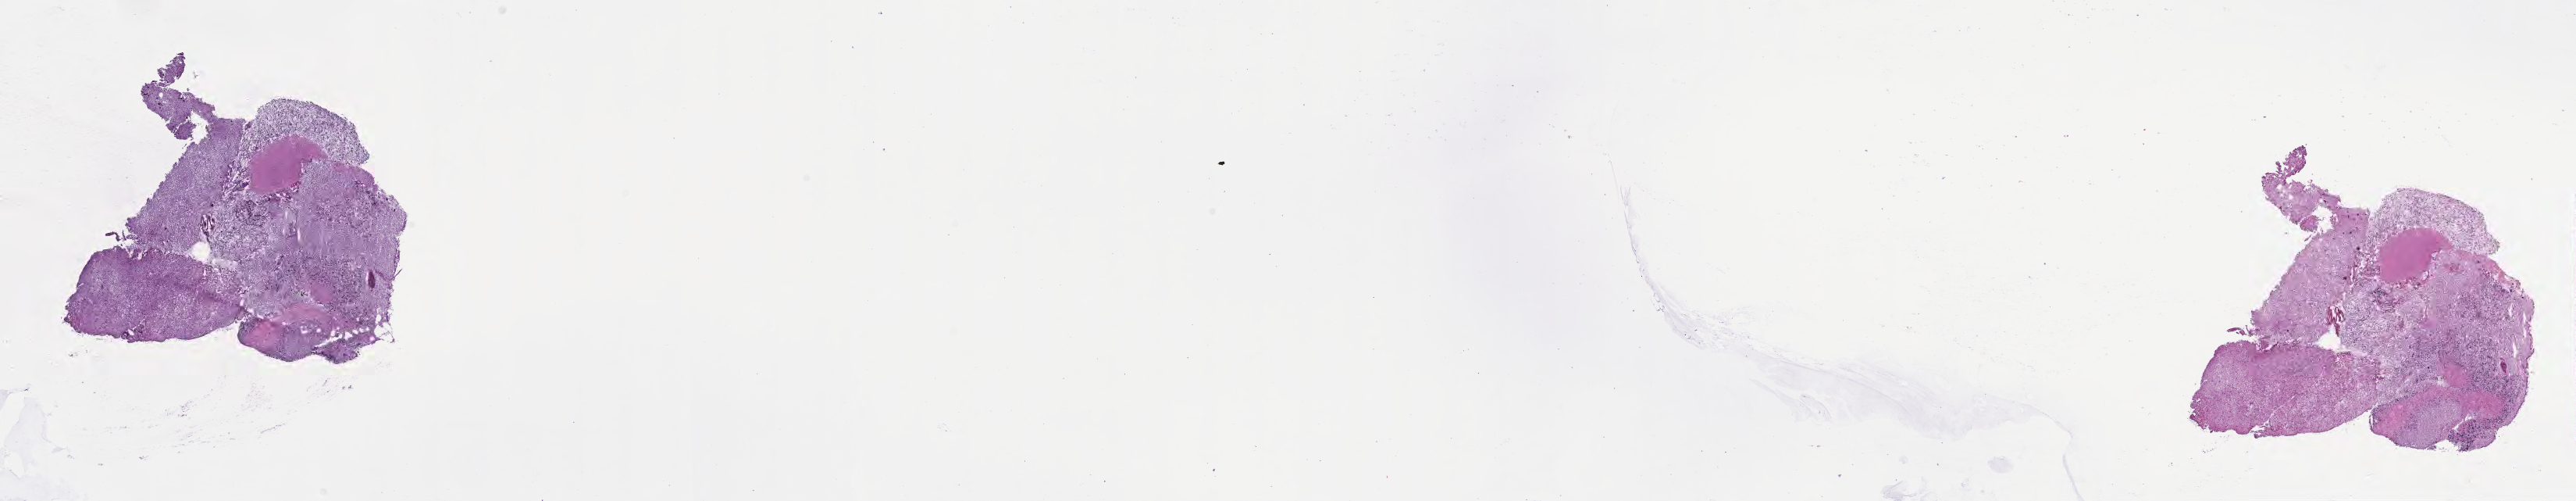
Whole-slide image, H&E stain of tumor tissue from the brain, shown as a low-resolution overview of the whole scanned area (about 26.7 x 5.2 mm), frozen section (OCT-embedded). Male patient, age 40 months (3 years 4 months).
Recorded diagnosis: Glioma, malignant.